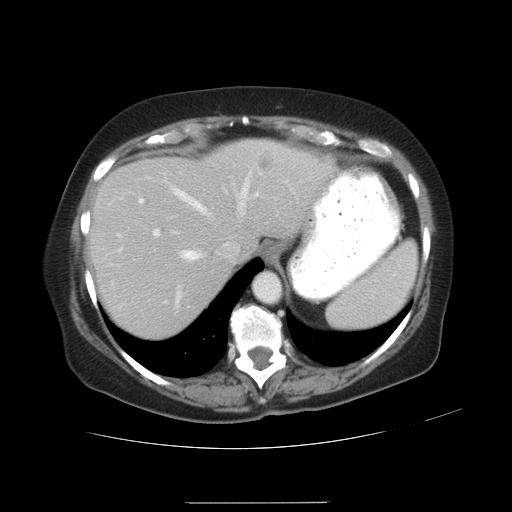
Contrast-enhanced abdominal CT, one axial slice. 120 kVp. Intravenous contrast given. Soft-tissue window (W 400 / L 40 HU). 7.5 mm slice thickness. 512 × 512 image matrix. Female patient, age 65 years. Case-level facts recorded for this patient, not image findings: diagnosis: colorectal cancer liver metastases, imaged before liver resection.
Outlined on this slice (expert manual segmentation):
- hepatic veins: bounding box [x1, y1, x2, y2] px = [108, 172, 251, 309]
- liver: [92, 143, 325, 338]
- planned liver remnant (the part of the liver to remain after resection): [92, 152, 239, 338]
- portal vein (with intrahepatic branches): [117, 228, 160, 252]
- liver metastasis: [261, 158, 273, 173]